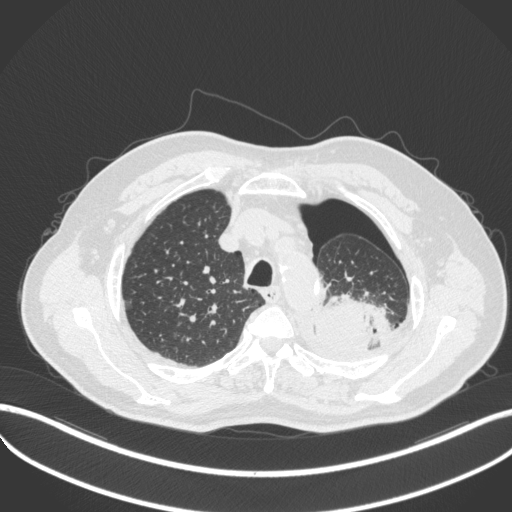
Chest CT, one axial slice; position 401 of 466 along the scan axis; 120 kVp; lung window (W 1500 / L -600 HU); 512 × 512 image matrix, field of view 400 × 400 mm. Male patient, age 76 years. Case-level facts recorded for this patient, not image findings: clinical TNM (as recorded): T3 N0 M1b.
Outlined on this slice (rectangle marked by the reading radiologist):
- lung tumour (recorded histology: adenocarcinoma): bounding box (x1, y1, x2, y2) in pixels: (312, 291, 394, 357)